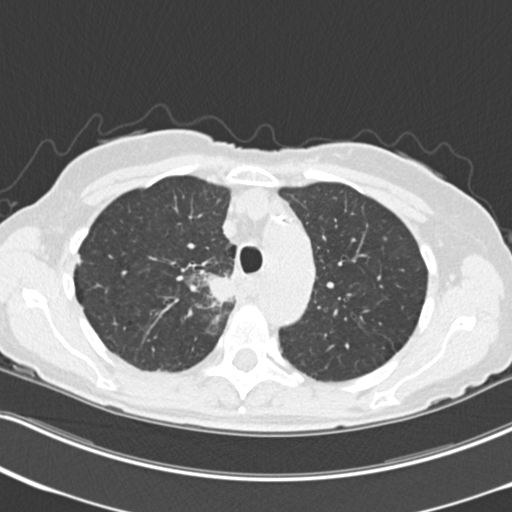
Low-dose screening chest CT, axial slice; third annual screen; lung window (W 1500 / L -600 HU); 2 mm slice thickness; 120 kVp; slice 58 of 226 in the series; 512 × 512 image matrix. Female participant, aged 68 years at enrolment. Current smoker at enrolment.
Expert-annotated lung lesion, box from (x=196, y=267) to (x=249, y=323) px. Screening reader's record for this exam (one nodule recorded; not confirmed to be the boxed lesion): non-calcified nodule or mass ≥4 mm, right upper lobe, 31 × 29 mm, poorly defined margins, soft tissue attenuation, pre-existing on the prior screen: no.